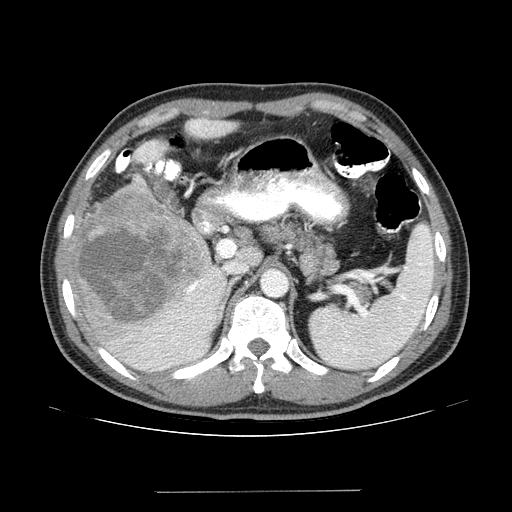
Contrast-enhanced abdominal CT (liver protocol), one axial slice. Position 87 of 131 along the scan axis. Reconstruction kernel STANDARD. 100 kVp. One of 2 acquisitions stored at this slice position. Soft-tissue window (W 400 / L 40 HU). 512 × 512 image matrix, field of view 380 × 380 mm. From the clinical record (not read from this slice): diagnosis: hepatocellular carcinoma (patient treated with transarterial chemoembolisation; whether this scan precedes or follows treatment is not stated here); TNM stage (as recorded): Stage-I; Child-Pugh class: A; tumour nodularity: uninodular; tumour size: 10.3 cm.
Annotated regions visible in this slice (semi-automatic segmentation, software-assisted and operator-edited):
- liver parenchyma outside the tumour (the mass and vessels are separate outlines, so this box may not span the whole liver): box from (x=62, y=120) to (x=236, y=372) px
- mass: (x=67, y=186)–(x=210, y=327)
- liver vessels: (x=152, y=282)–(x=211, y=370)